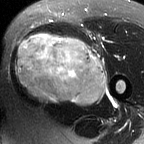
MRI of an extremity soft-tissue mass, one axial slice; position 34 of 60 along the scan axis; T2-weighted fat-saturated; MR volume resampled by the dataset authors to the PET/CT grid (not the native acquisition matrix); 144 × 144 image matrix, field of view 141 × 141 mm. Female patient. Case-level facts recorded for this patient, not image findings: histological type: pleiomorphic leiomyosarcoma; grade: intermediate; site of the primary tumour: left thigh.
Structures marked on this image (expert contour drawn on MRI and transferred to this co-registered scan by the dataset authors):
- gross tumour volume including surrounding oedema: box from (x=15, y=33) to (x=105, y=105) px
- gross tumour volume (mass): (x=15, y=35)–(x=105, y=105)